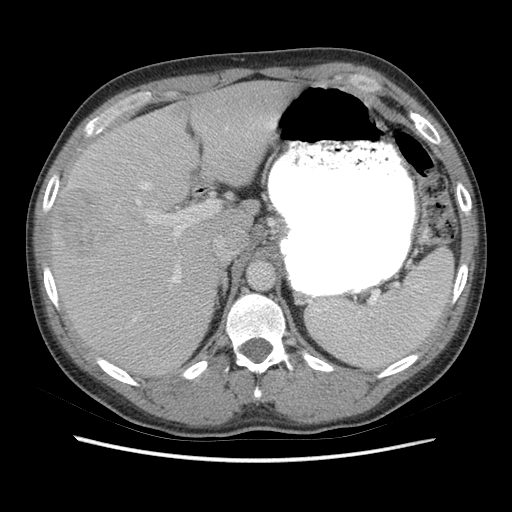
Contrast-enhanced abdominal CT (liver protocol), one axial slice. Slice 45 of 73 in the series (ordered by position). 140 kVp. Soft-tissue window (W 400 / L 40 HU). 2.5 mm slice thickness. 512 × 512 image matrix, field of view 360 × 360 mm. Case-level facts recorded for this patient, not image findings: diagnosis: hepatocellular carcinoma (patient treated with transarterial chemoembolisation; whether this scan precedes or follows treatment is not stated here); TNM stage (as recorded): Stage-IIIA; Child-Pugh class: A; tumour size: 6.6 cm.
Annotated regions visible in this slice (semi-automatically segmented with operator editing):
- liver parenchyma outside the tumour (the mass and vessels are separate outlines, so this box may not span the whole liver): bounding box <50,80,296,374> (left, top, right, bottom; pixels)
- mass: <55,187,114,257>
- liver vessels: <132,119,276,322>